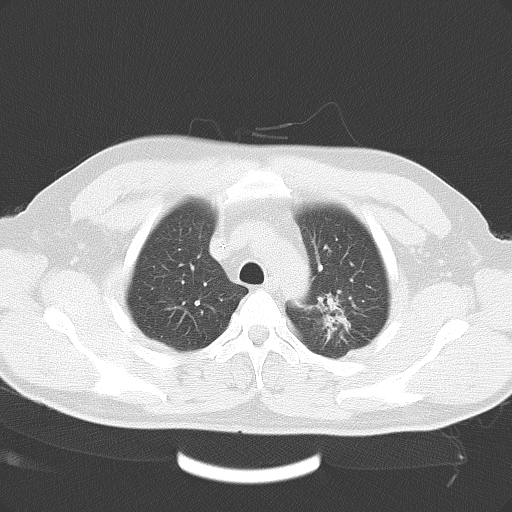
Chest CT, one axial slice. Slice 31 of 41 in the series (ordered by position). Reconstruction kernel B70f. Lung window (W 1500 / L -600 HU). 5 mm slice thickness. 512 × 512 image matrix, field of view 362 × 362 mm. Male patient, age 45 years. Case-level facts recorded for this patient, not image findings: clinical TNM (as recorded): T2 N0 M0.
Annotated regions visible in this slice (bounding box drawn by a radiologist):
- lung tumour (recorded histology: adenocarcinoma): bounding box (x1, y1, x2, y2) in pixels: (310, 292, 361, 350)